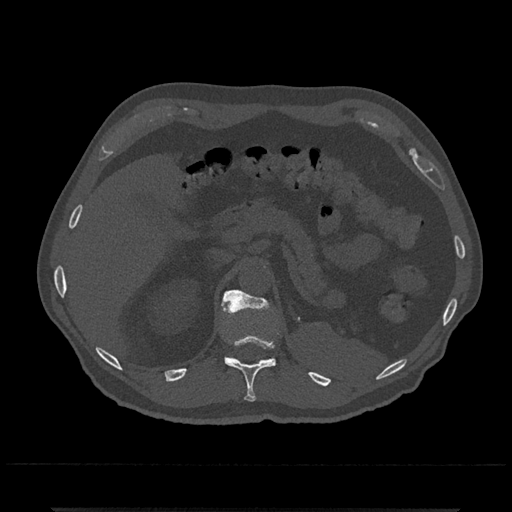
CT including the spine, one axial slice. Slice 471 of 797 in the series (ordered by position). 120 kVp. Bone window (W 1800 / L 400 HU). 512 × 512 image matrix, field of view 393 × 393 mm. Patient: male, 67 years. Case-level facts recorded for this patient, not image findings: primary cancer: prostate.
Annotated regions visible in this slice (semi-automatic segmentation, software-assisted and operator-edited):
- T11 vertebra: box from (x=221, y=302) to (x=276, y=402) px
- T12 vertebra: (x=222, y=290)–(x=273, y=360)